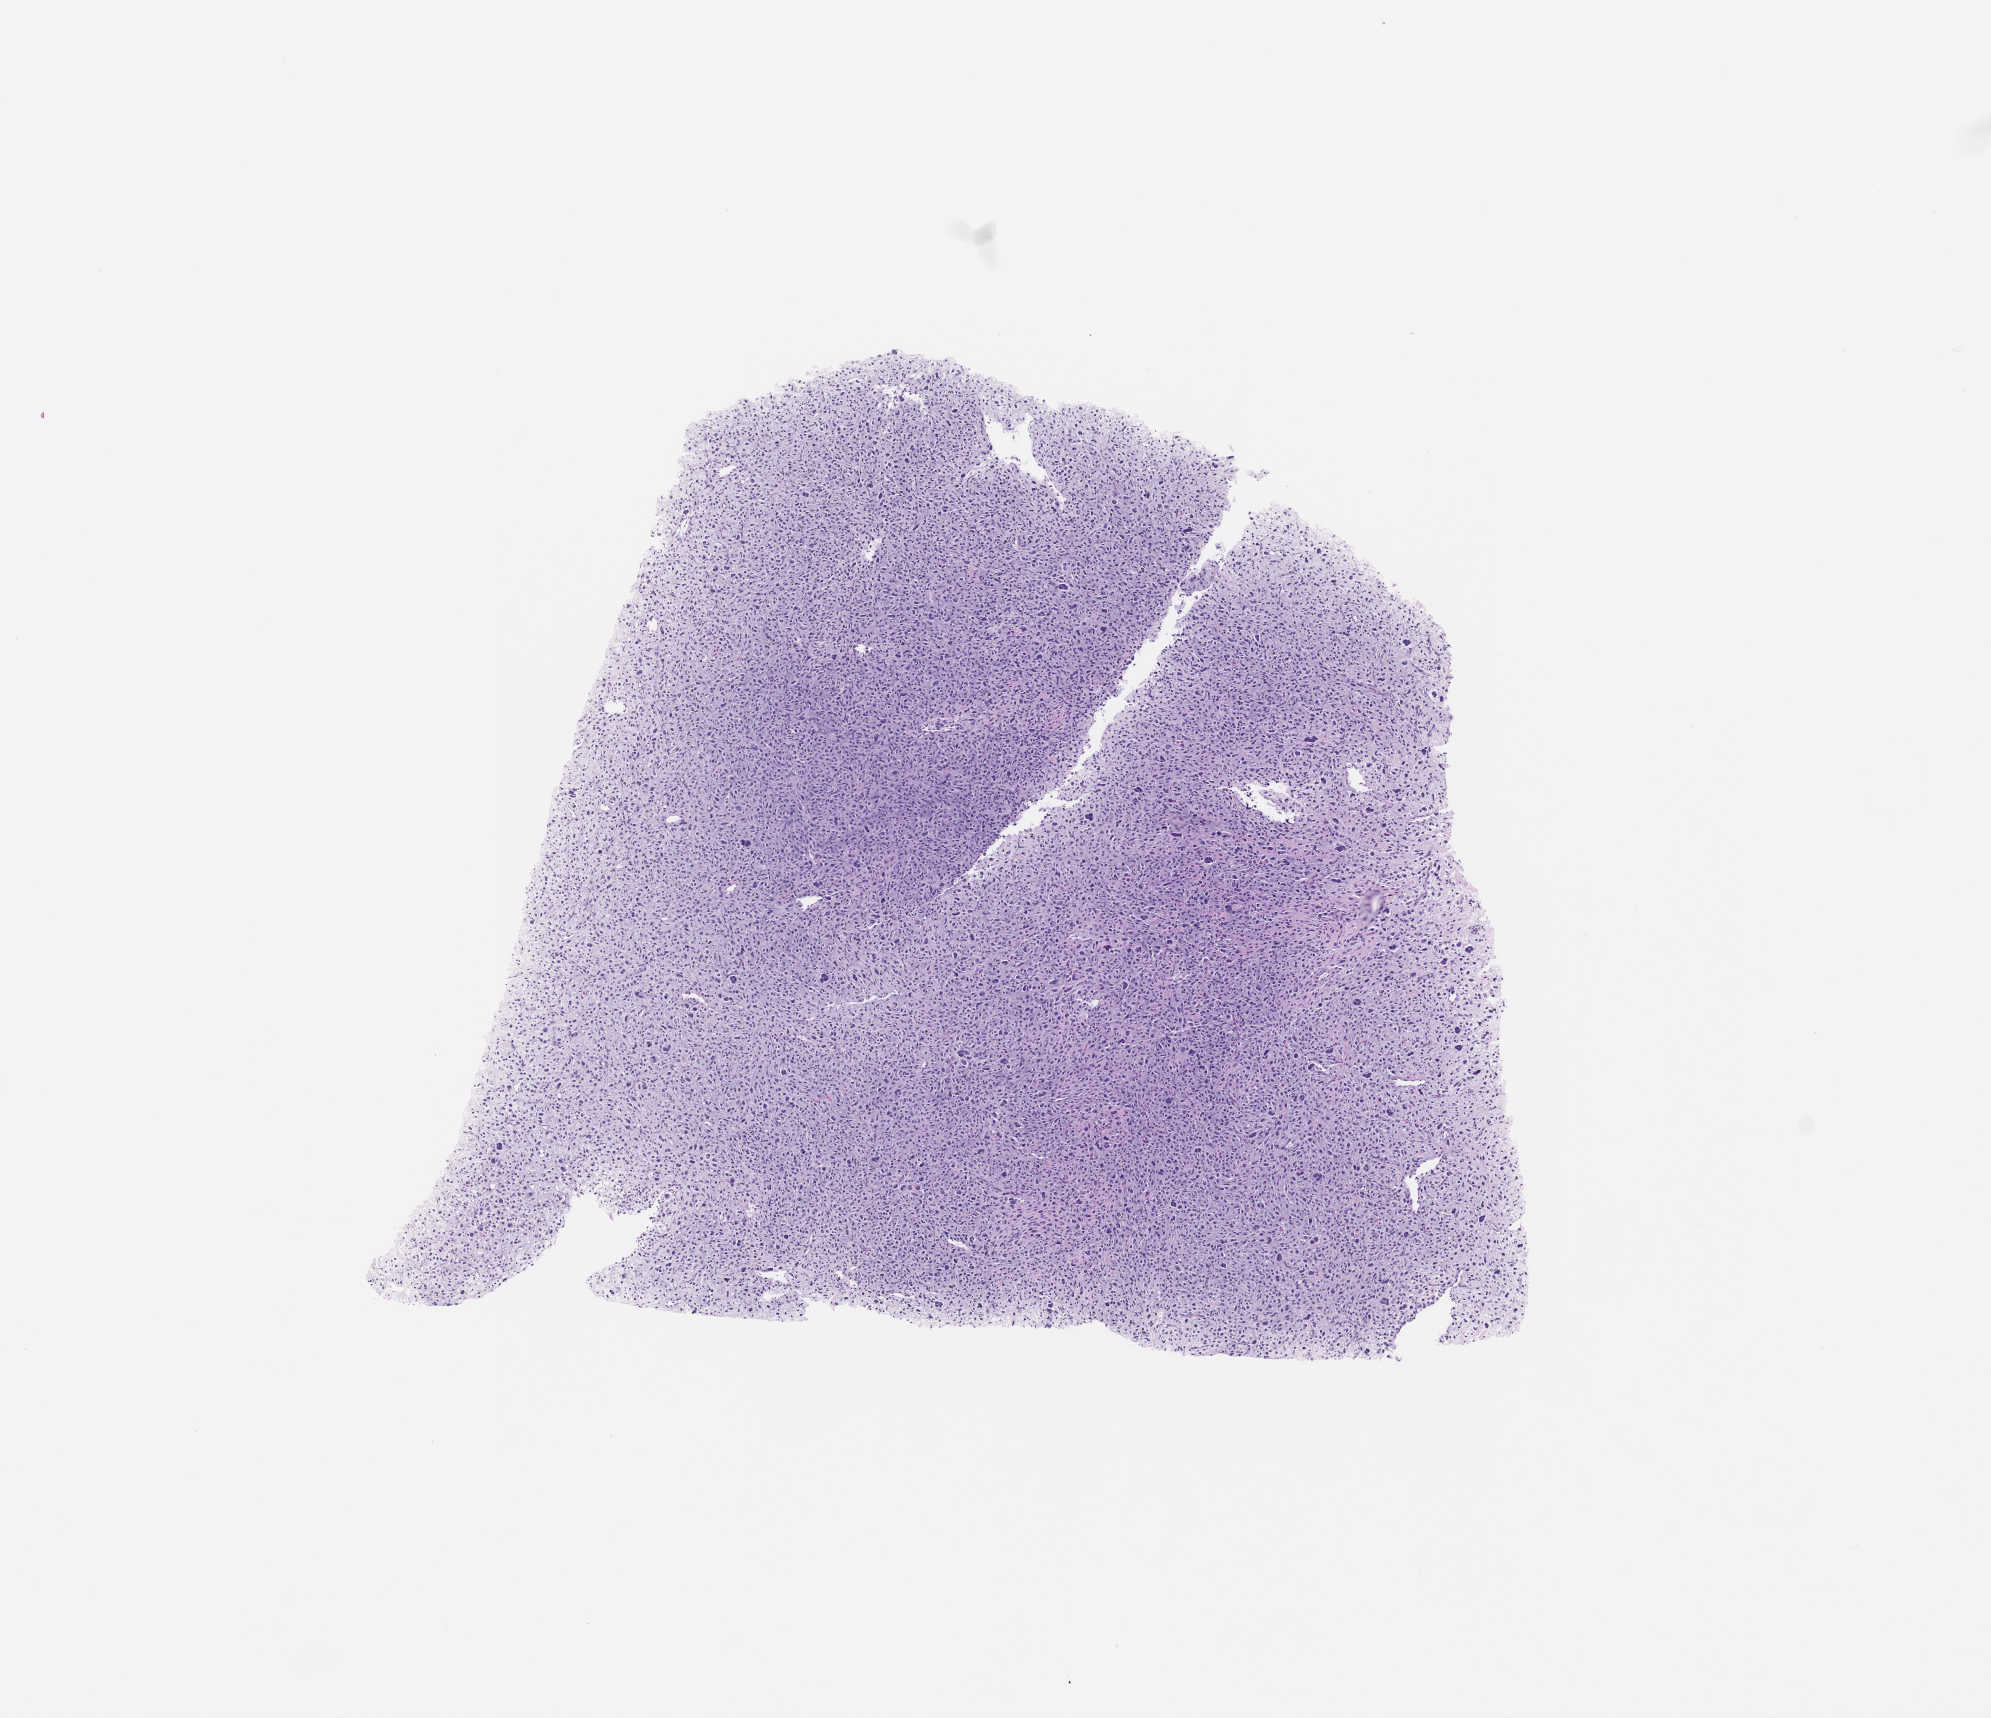
Whole-slide image, haematoxylin and eosin stain of the patient's (originator) tumor tissue, low-resolution overview of the scanned area, about 8.0 x 6.9 mm; formalin-fixed, paraffin-embedded (FFPE) tissue; originating tumor site category: musculoskeletal. Male patient, age 80 years.
- diagnosis: Myxofibrosarcoma